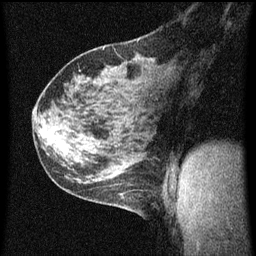
Breast MRI (dynamic contrast-enhanced), one sagittal slice; position 35 of 60 along the scan axis; dynamic contrast-enhanced series, image 2 of 3 at this slice position (ordered by acquisition); 1.5 T; TE 4.2 ms, TR 8 ms; 2 mm slice thickness; 256 × 256 image matrix, field of view 180 × 180 mm. Female patient, age 35 years.
Outlined on this slice (semi-automatically segmented with operator editing):
- analysis volume of interest (the breast-tissue region the enhancement analysis was run in; not a lesion): bounding box (x1, y1, x2, y2) in pixels: (106, 182, 145, 217)
- tumour enhancement mask (voxels above the 70 % enhancement threshold inside the analysis volume of interest): (120, 184, 133, 187)